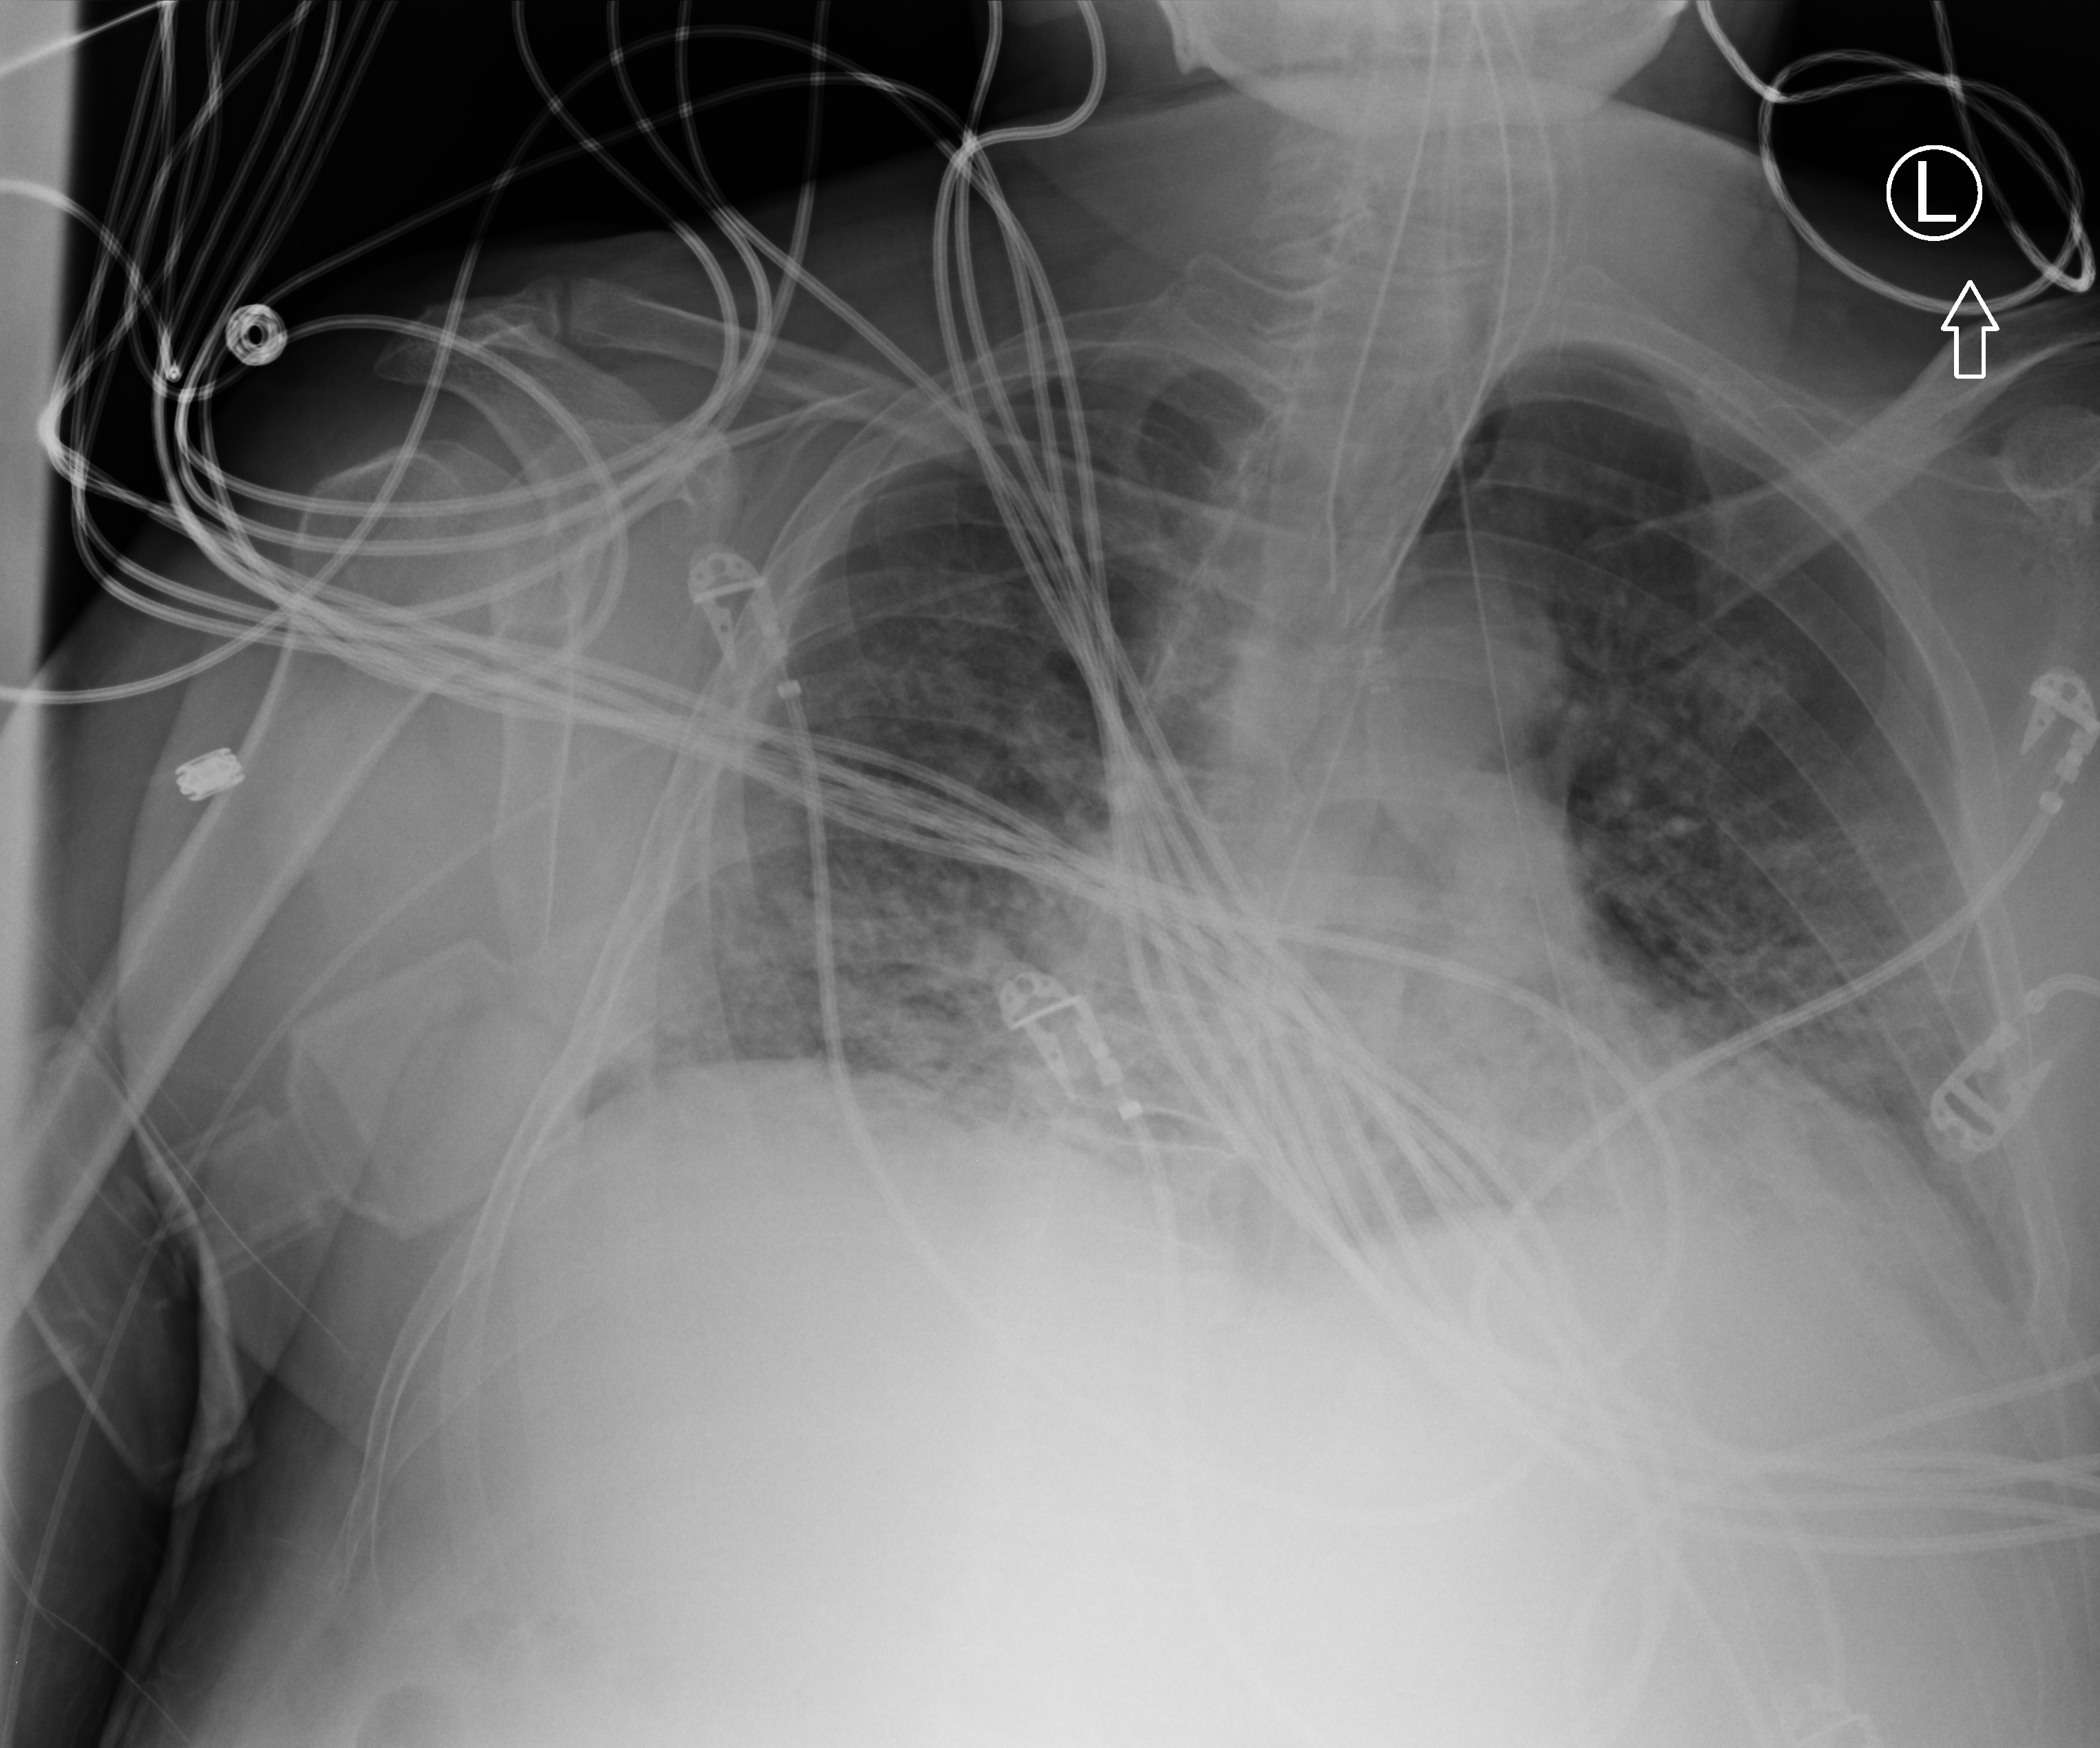
Bedside chest radiograph (computed radiography); anteroposterior (AP) projection. Patient hospitalised with COVID-19; male, aged 60–74 years.
From the hospital-stay record, not from the radiograph (when in the stay this image was taken is not recorded):
- length of hospital stay: 19 days
- admitted to intensive care during this hospital stay: yes
- mechanically ventilated during this hospital stay: yes